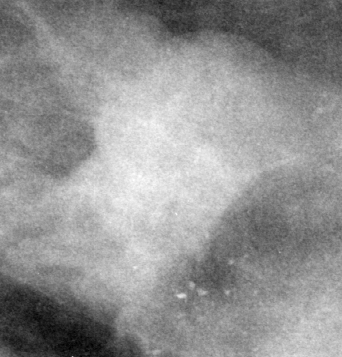
Crop from a digitized film mammogram around one marked abnormality, left breast, MLO view, BI-RADS breast density category 4 (scale 1–4).
Mass, shape lobulated, margins obscured; BI-RADS assessment category 3; subtlety rating 5 on a 1 (subtle) to 5 (obvious) scale; pathology (as recorded): benign.